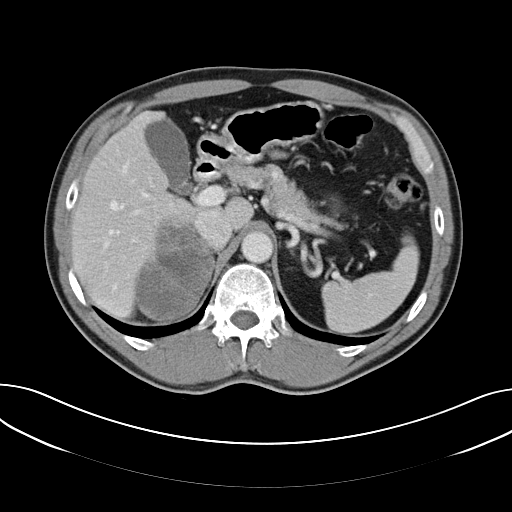
Contrast-enhanced abdominal CT, one axial slice. Slice 39 of 61 in the series (ordered by position). Reconstruction kernel B40f. Soft-tissue window (W 400 / L 40 HU). 5 mm slice thickness. 512 × 512 image matrix, field of view 372 × 372 mm. Male patient, age 57 years. From the clinical record (not read from this slice): diagnosis: adrenocortical carcinoma; tumour side: right adrenal.
Structures marked on this image (semi-automatic segmentation, software-assisted and operator-edited):
- mass: bounding box (x1, y1, x2, y2) in pixels: (136, 223, 212, 319)